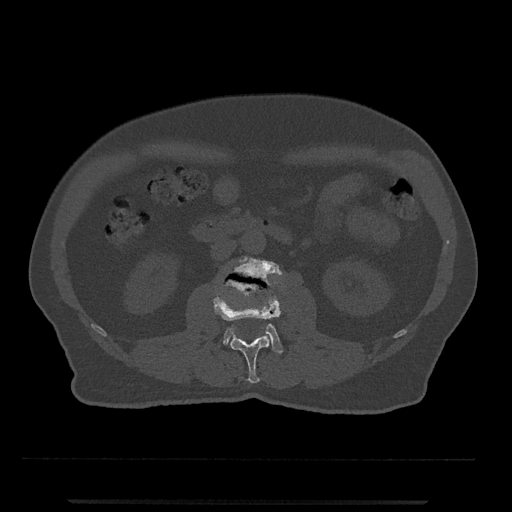
CT including the spine, one axial slice; slice 242 of 797 in the series (ordered by position); reconstruction kernel Br40s/3; bone window (W 1800 / L 400 HU); 0.5 mm slice thickness; 512 × 512 image matrix. Male patient, age 63 years. From the clinical record (not read from this slice): primary cancer: prostate.
Outlined on this slice (semi-automatic segmentation, software-assisted and operator-edited):
- L2 vertebra: bounding box <213,268,281,383> (left, top, right, bottom; pixels)
- L3 vertebra: <223,256,283,353>